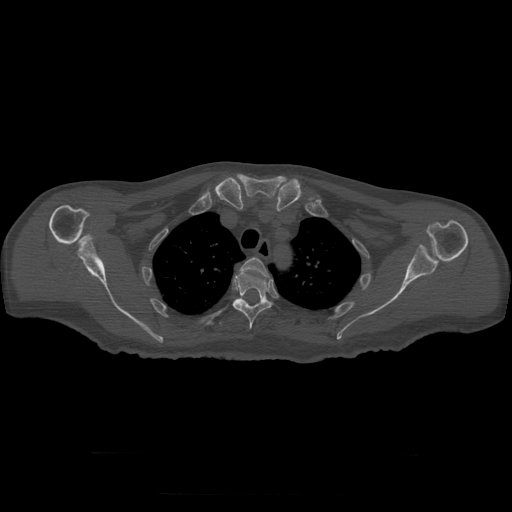
CT including the spine, one axial slice; reconstruction kernel STANDARD; bone window (W 1800 / L 400 HU); 1.25 mm slice thickness; 512 × 512 image matrix, field of view 510 × 510 mm. Patient age 73 years. Case-level facts recorded for this patient, not image findings: primary cancer: prostate.
Outlined on this slice (semi-automatically segmented with operator editing):
- T3 vertebra: bounding box [x1, y1, x2, y2] px = [240, 258, 269, 277]
- T4 vertebra: [233, 272, 272, 330]
- T5 vertebra: [220, 299, 241, 325]